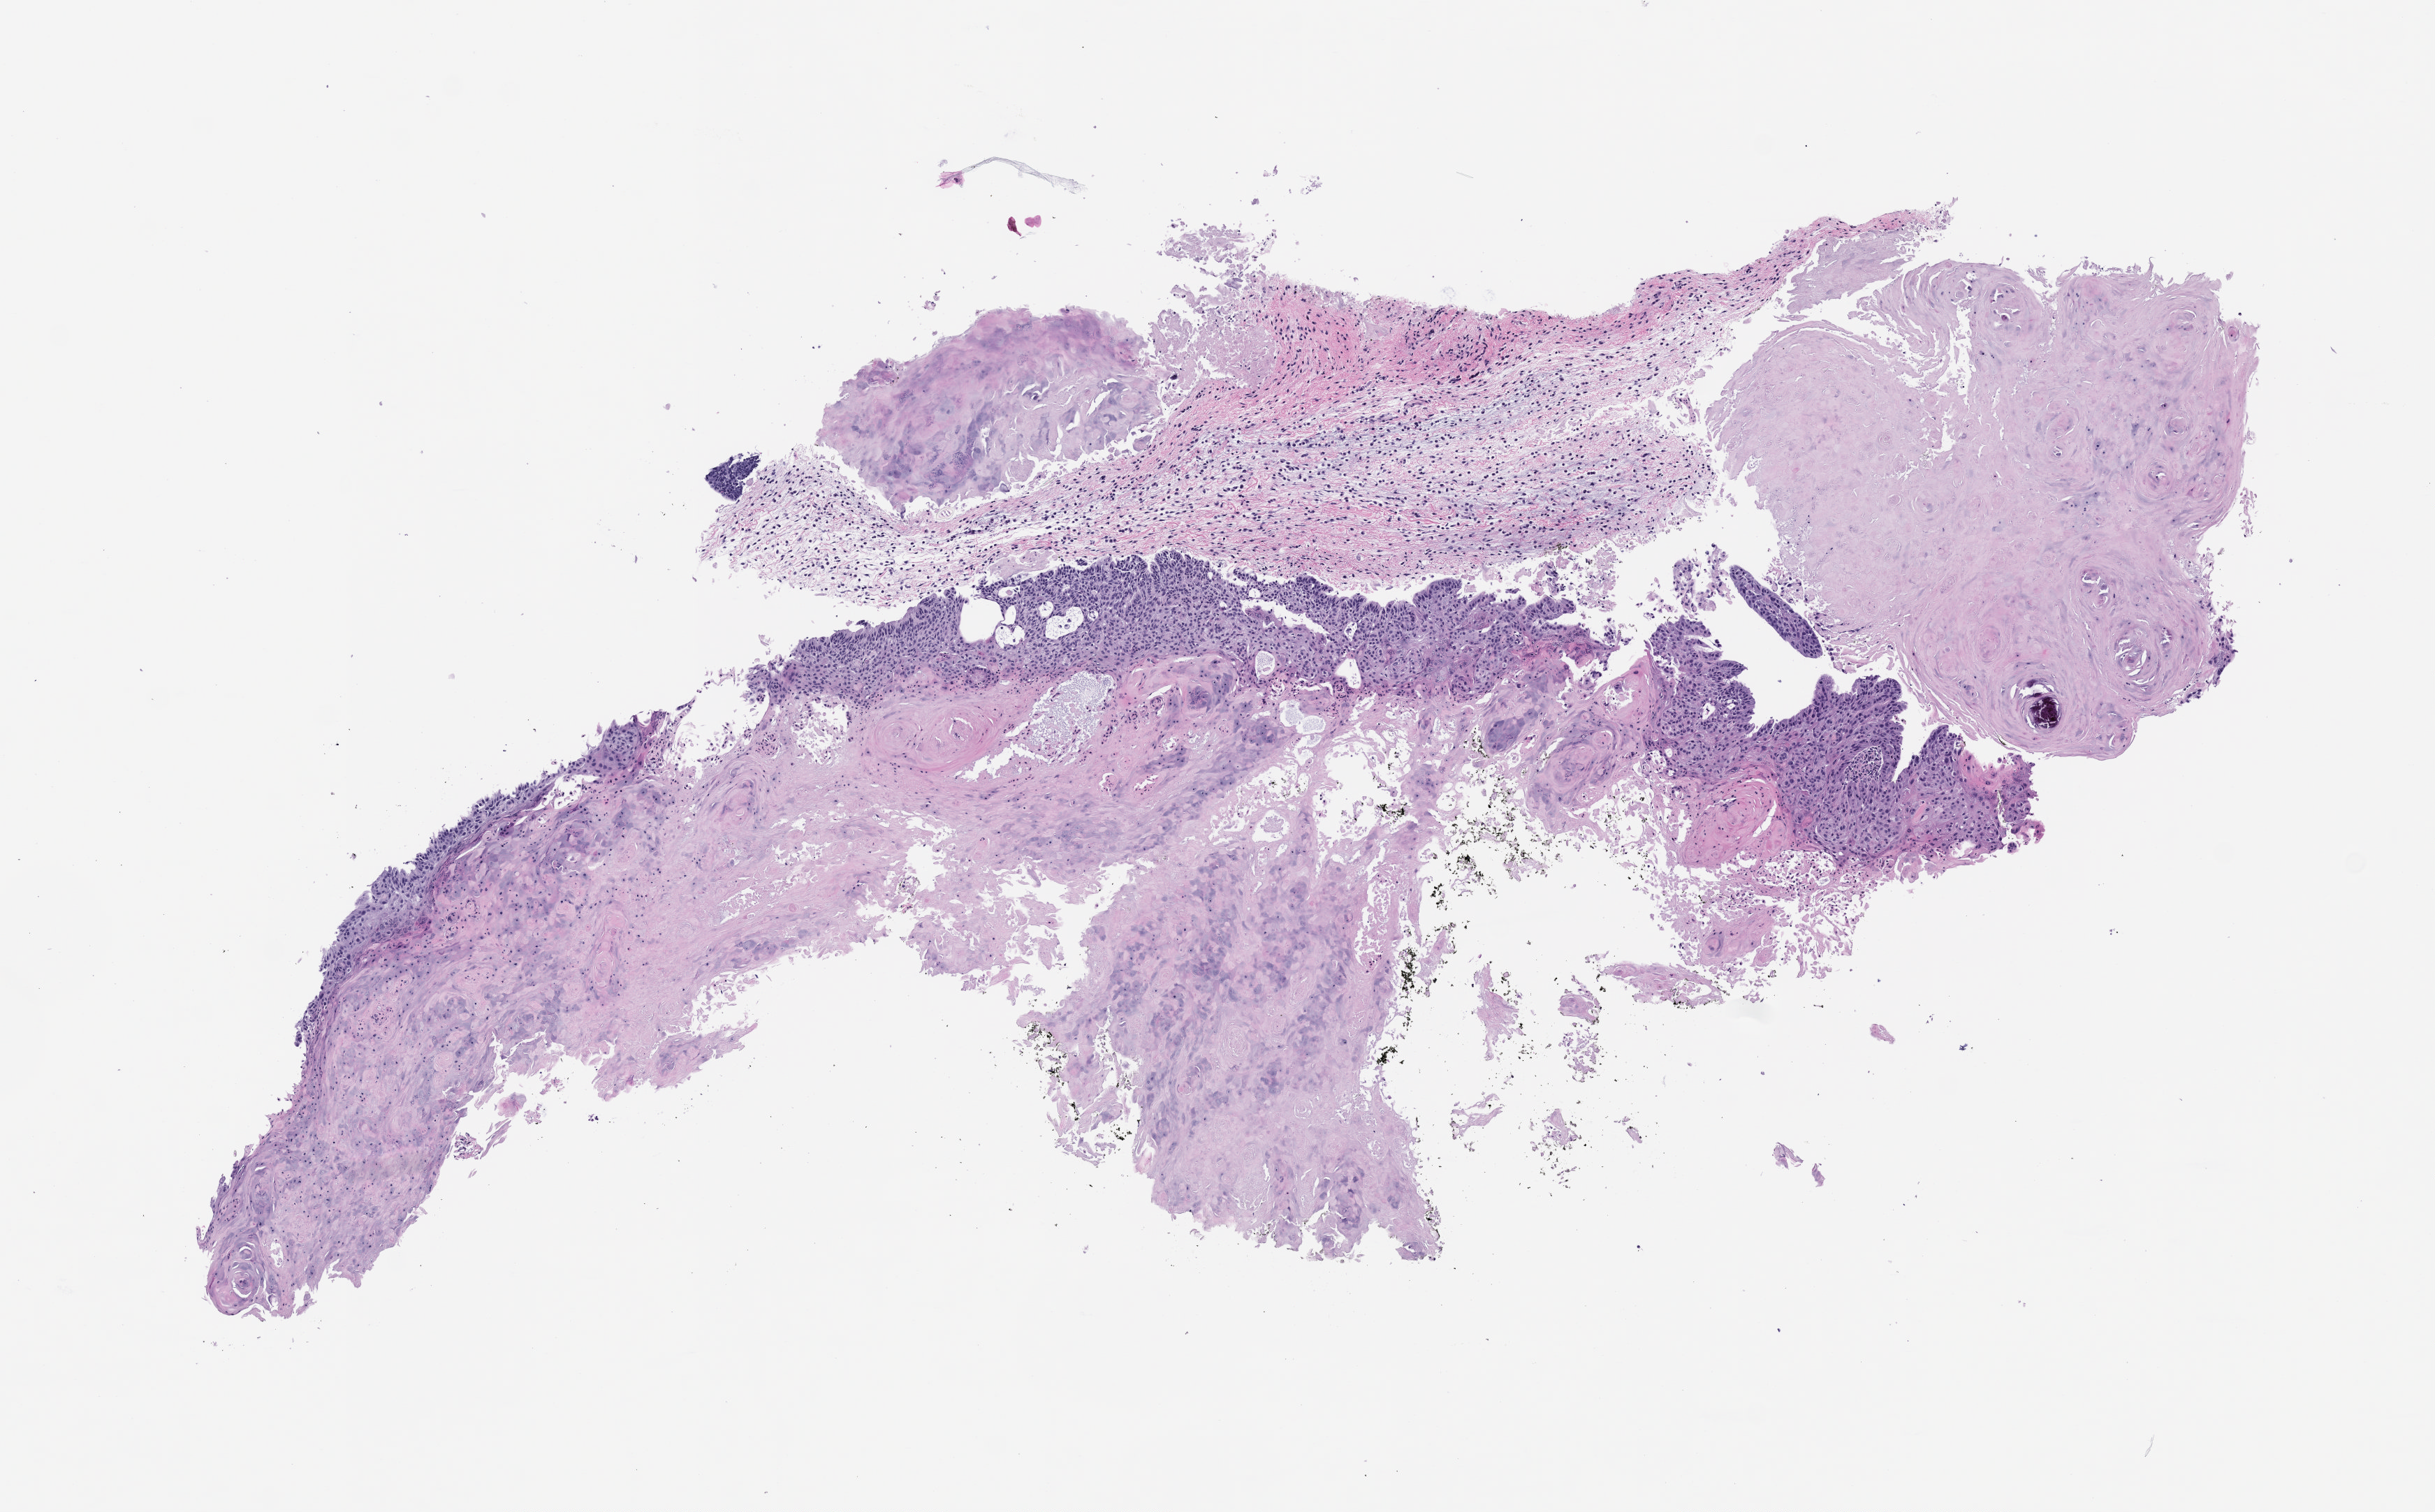
H&E whole-slide image of a patient-derived xenograft (PDX) tumor grown in a mouse, low-resolution overview of the scanned area, about 7.0 x 4.4 mm. Formalin-fixed paraffin-embedded section. Originating tumor site category: larynx.
Originating patient diagnosis: Head and Neck Squamous Cell Carcinoma.